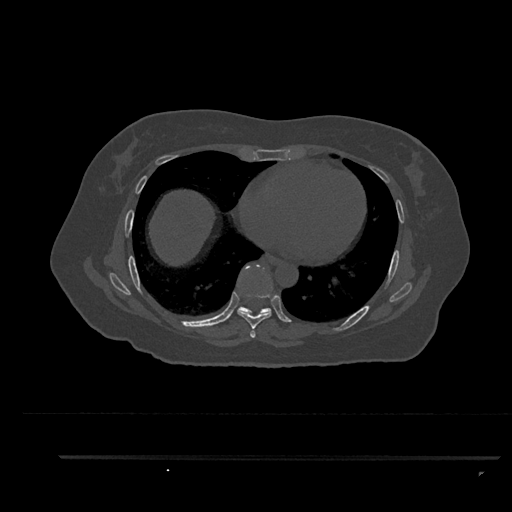
CT including the spine, one axial slice. 120 kVp. Bone window (W 1800 / L 400 HU). 0.5 mm slice thickness. 512 × 512 image matrix, field of view 408 × 408 mm. Patient: female, 44 years. Case-level facts recorded for this patient, not image findings: primary cancer: renal.
Annotated regions visible in this slice (semi-automatic segmentation, software-assisted and operator-edited):
- T6 vertebra: box from (x=251, y=335) to (x=255, y=337) px
- T7 vertebra: (x=237, y=264)–(x=273, y=338)
- T8 vertebra: (x=237, y=274)–(x=271, y=316)